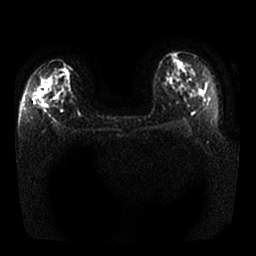
Breast MRI, one axial slice; slice 13 of 25 in the series (ordered by position); diffusion-weighted series; image 2 of 4 stored at this slice position (different b-values; order by instance number); 1.5 T; 256 × 256 image matrix, field of view 340 × 340 mm. Female patient.
Structures marked on this image (outlined manually by an expert reader):
- tumour on diffusion-weighted imaging: bounding box [x1, y1, x2, y2] px = [38, 88, 53, 100]